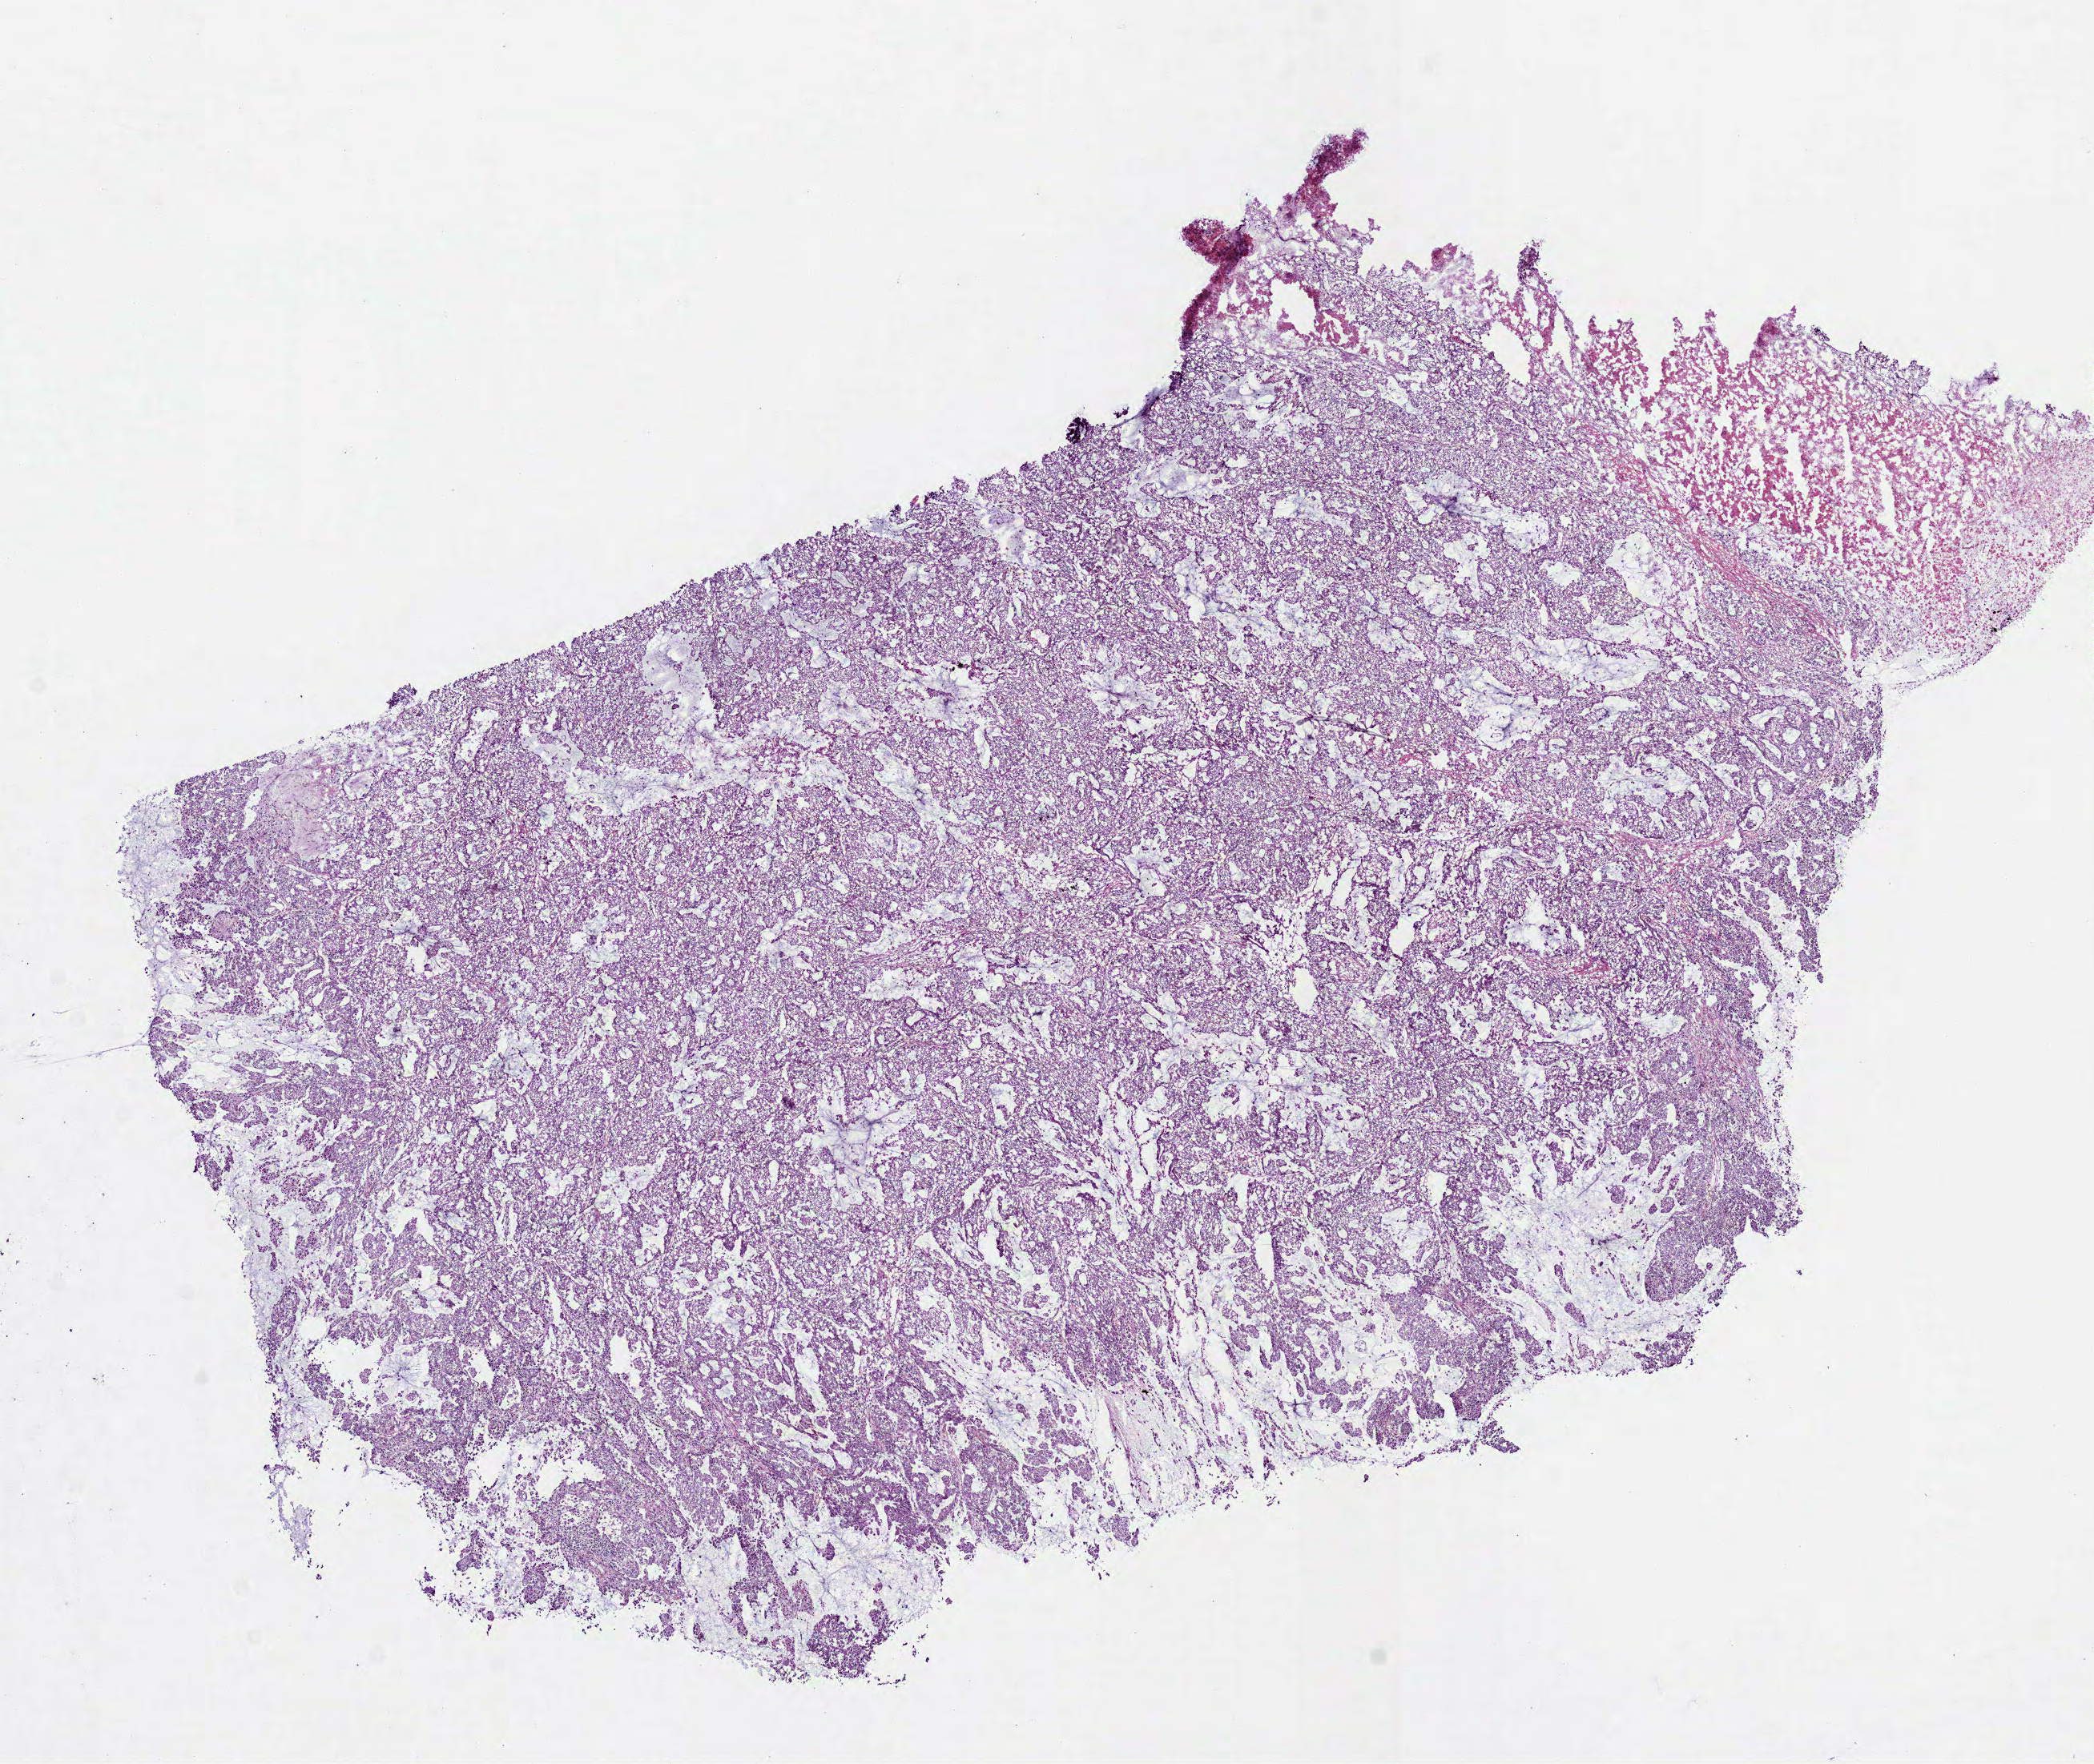
Whole-slide histology image, H&E, shown as a low-resolution overview of the whole scanned area (about 10.5 x 8.9 mm), frozen section from the top of the tissue portion, sample: primary tumour, lung. Male patient; age at initial diagnosis 58 years. Pathologist review of this section (percent, as recorded): tumour cells 95%, tumour nuclei 80%, normal cells 0%, stromal cells 0%, necrosis 5%. Inflammatory infiltration, as recorded: lymphocyte infiltration 10%, monocyte infiltration 1%, neutrophil infiltration 5%.
AJCC pathologic stage: IIIA (6th edition). Pathologic diagnosis: Mucinous adenocarcinoma.